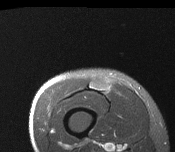
MRI of an extremity soft-tissue mass, one axial slice. Slice 30 of 116 in the series (ordered by position). T2-weighted fat-saturated. MR volume resampled by the dataset authors to the PET/CT grid (not the native acquisition matrix). 3.27 mm slice thickness. 175 × 152 image matrix. Male patient. Case-level facts recorded for this patient, not image findings: histological type: pleiomorphic leiomyosarcoma; grade: intermediate; site of the primary tumour: right thigh.
Structures marked on this image (expert contour drawn on MRI and transferred to this co-registered scan by the dataset authors):
- gross tumour volume including surrounding oedema: box from (x=92, y=81) to (x=109, y=93) px